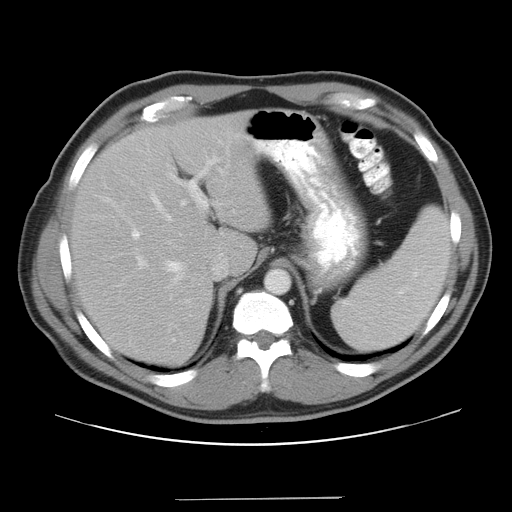
Contrast-enhanced abdominal CT, one axial slice; slice 29 of 37 in the series (ordered by position); reconstruction kernel STANDARD; 120 kVp; intravenous contrast given; soft-tissue window (W 400 / L 40 HU); 7.5 mm slice thickness; 512 × 512 image matrix, field of view 400 × 400 mm. Male patient, age 46 years. From the clinical record (not read from this slice): diagnosis: colorectal cancer liver metastases, imaged before liver resection; multiple liver metastases: yes; largest metastasis: 1 cm.
Outlined on this slice (manually delineated by an expert):
- hepatic veins: bounding box [x1, y1, x2, y2] px = [152, 169, 223, 288]
- liver: [73, 116, 268, 364]
- planned liver remnant (the part of the liver to remain after resection): [73, 116, 268, 364]
- portal vein (with intrahepatic branches): [132, 156, 220, 342]
- liver metastasis: [113, 162, 120, 167]